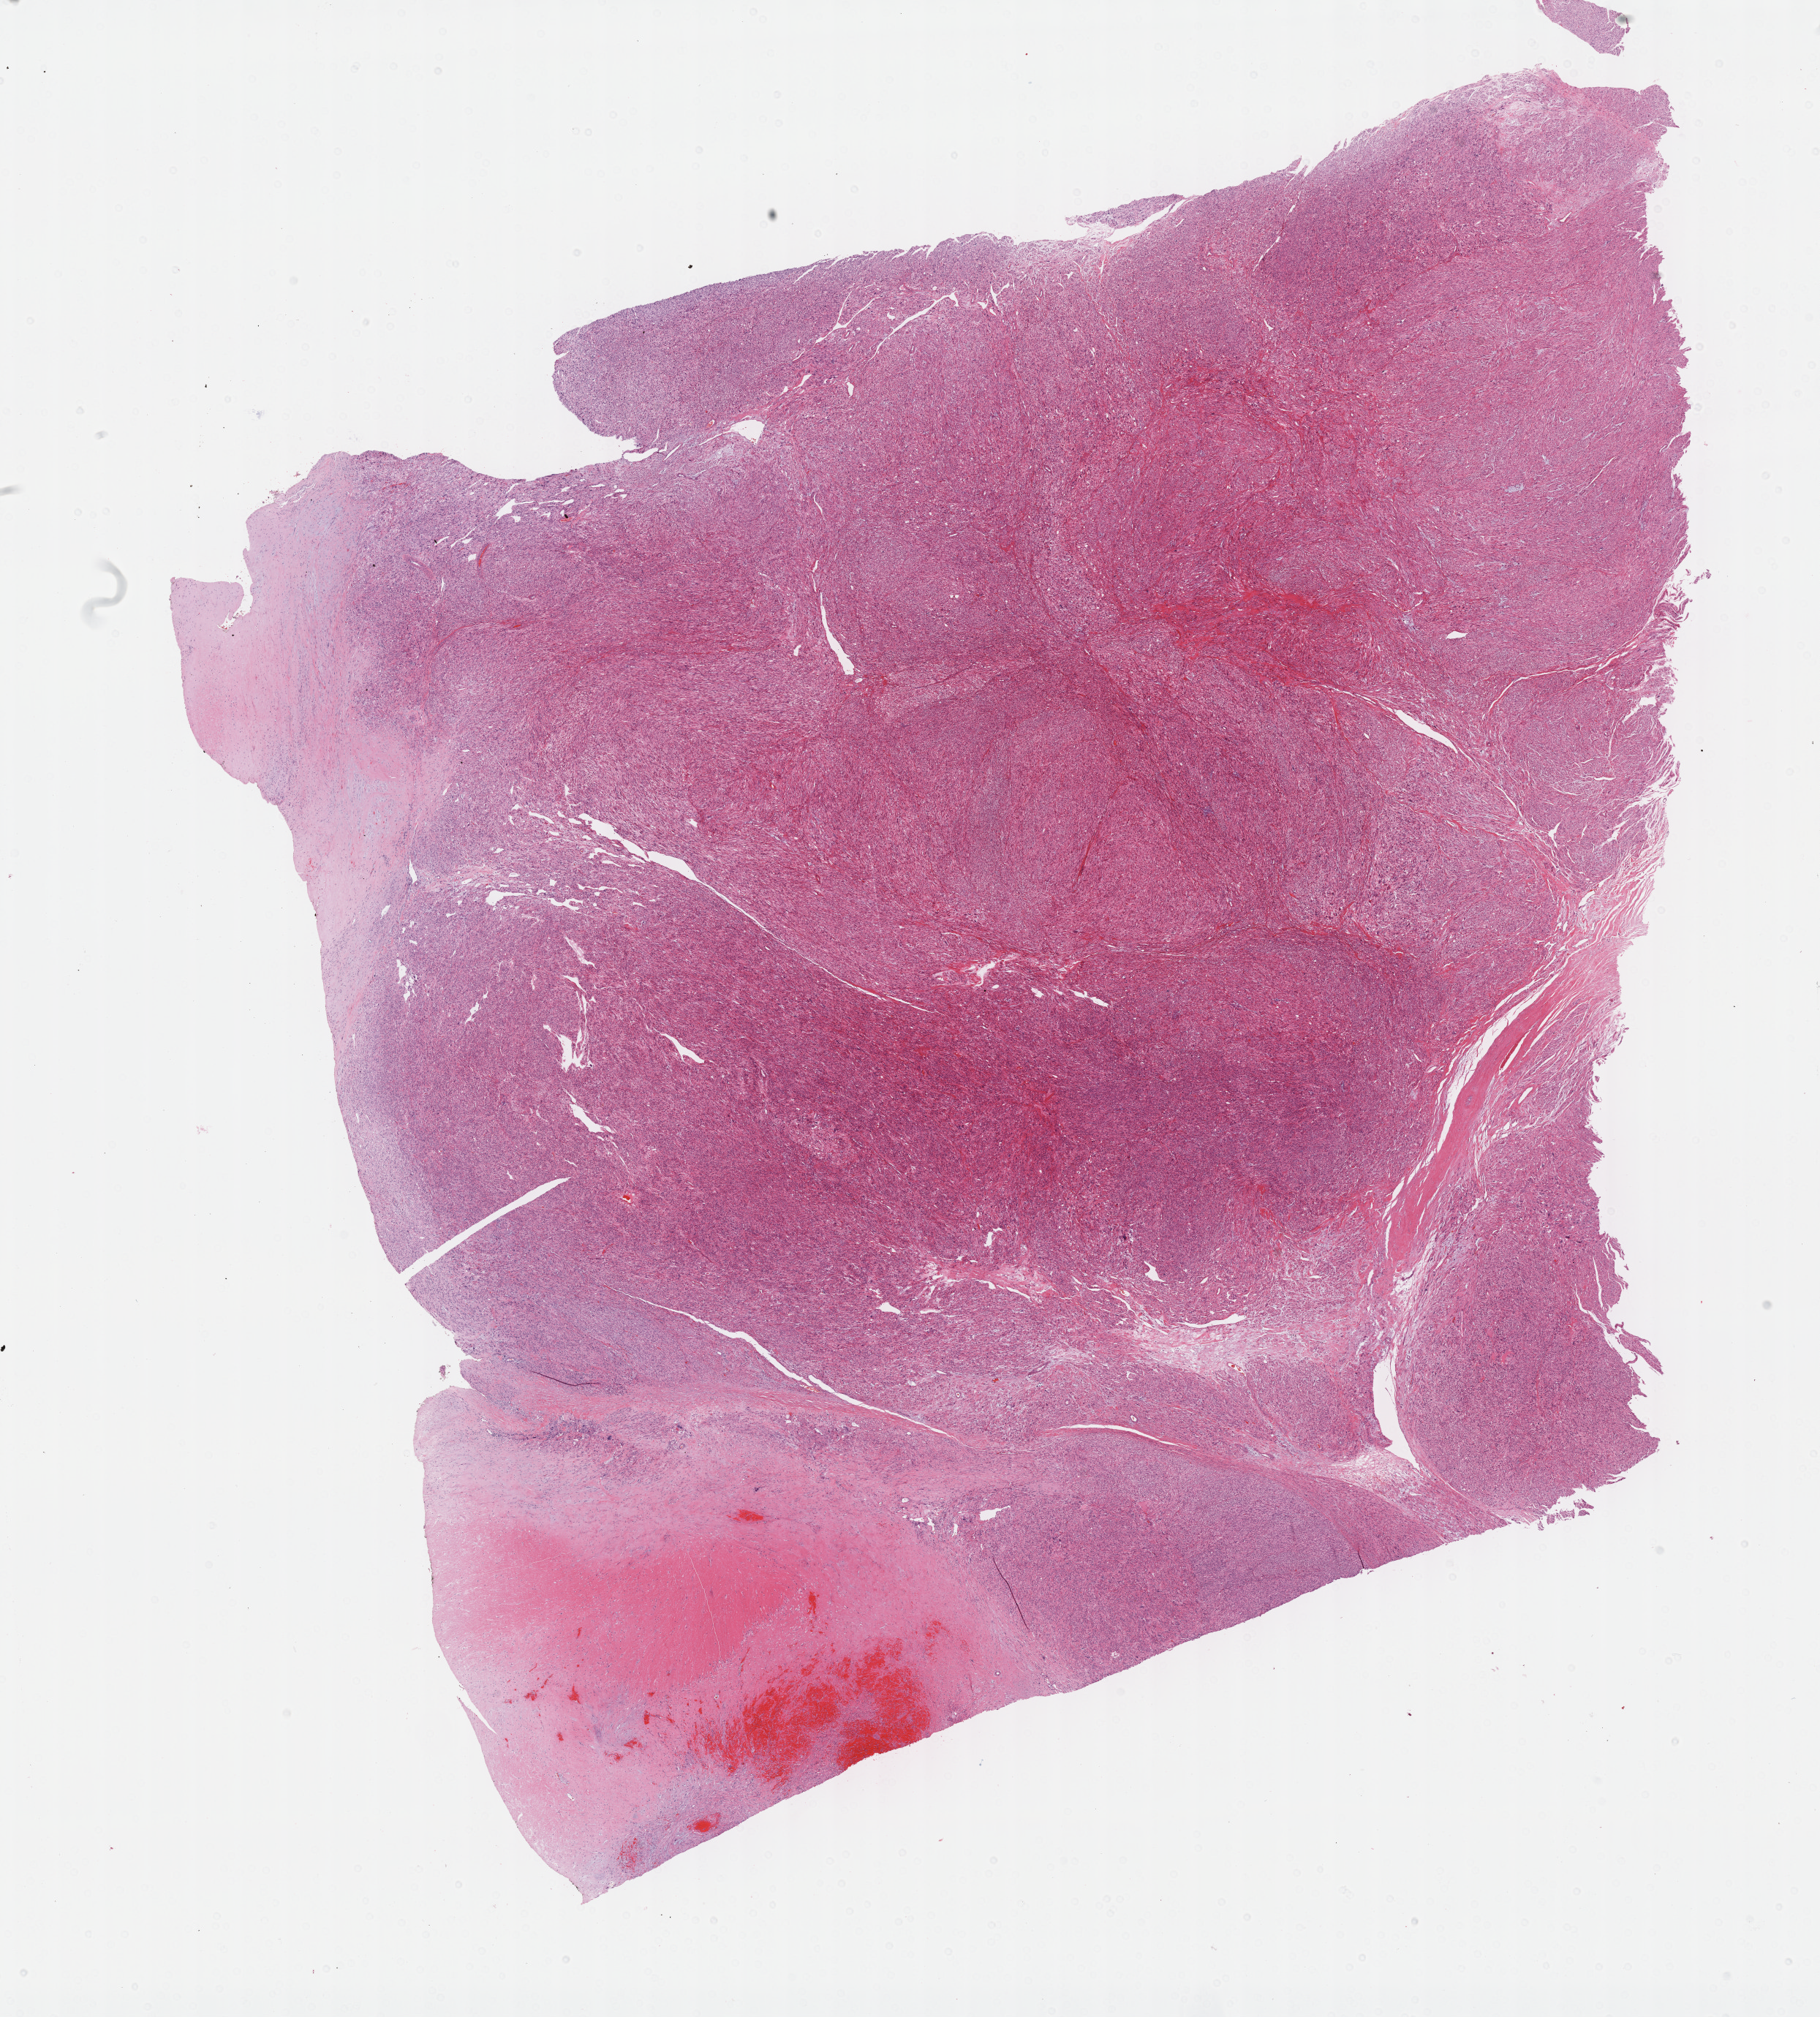
H&E-stained whole-slide image — low-resolution overview of the scanned area, about 20.1 x 22.3 mm. Formalin-fixed paraffin-embedded (FFPE) diagnostic section. Connective, subcutaneous and other soft tissues, primary tumour sample. Patient: female, age at initial diagnosis 56 years.
Diagnosis: Leiomyosarcoma, NOS.